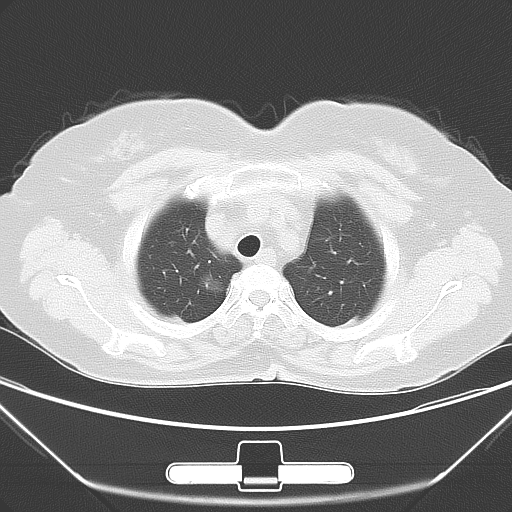
Chest CT, one axial slice; position 47 of 55 along the scan axis; lung window (W 1500 / L -600 HU); 5 mm slice thickness; 512 × 512 image matrix. Female patient, age 63 years. Case-level facts recorded for this patient, not image findings: clinical TNM (as recorded): T1a N0 M0; histopathological grade: G1.
Annotated regions visible in this slice (rectangle marked by the reading radiologist):
- lung tumour (recorded histology: adenocarcinoma): bounding box [x1, y1, x2, y2] px = [194, 269, 224, 296]